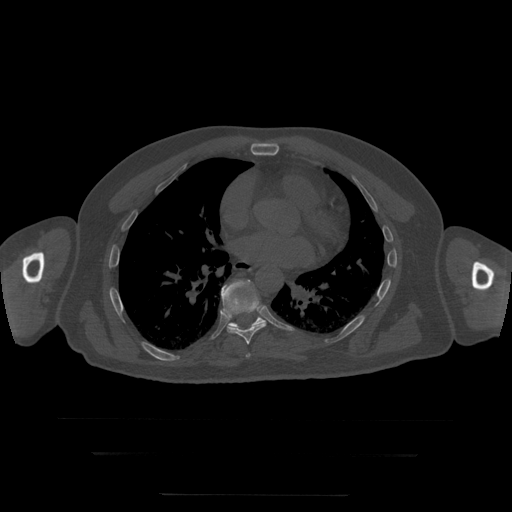
CT including the spine, one axial slice; slice 160 of 397 in the series (ordered by position); reconstruction kernel STANDARD; bone window (W 1800 / L 400 HU); 1.25 mm slice thickness; 512 × 512 image matrix. Patient age 73 years. From the clinical record (not read from this slice): primary cancer: prostate.
Annotated regions visible in this slice (semi-automatic segmentation, software-assisted and operator-edited):
- T7 vertebra: bounding box [x1, y1, x2, y2] px = [246, 354, 251, 358]
- T8 vertebra: [221, 280, 267, 345]
- T9 vertebra: [228, 288, 266, 329]